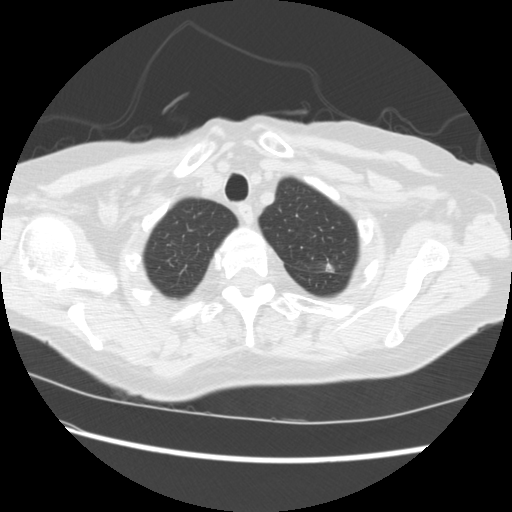
Low-dose screening chest CT, axial slice, baseline screening round, lung window (W 1500 / L -600 HU), 2.5 mm slice thickness, slice 32 of 224 in the series. Female participant, aged 74 years at enrolment. Former smoker at enrolment.
Expert-annotated lung lesion, bounding box (x1, y1, x2, y2) in pixels: (298, 250, 348, 286). The screening reader recorded 2 non-calcified nodules or masses ≥4 mm on this exam (left upper lobe, right lower lobe); which of them this box marks is not recorded. Official screen result: positive, change unspecified: nodule(s) >= 4 mm or enlarging nodule(s), mass(es), or other non-specific abnormalities suspicious for lung cancer. Later outcome: lung cancer diagnosed 309 days after this screen — non-small cell carcinoma, left upper lobe, stage IV (AJCC 6th edition).